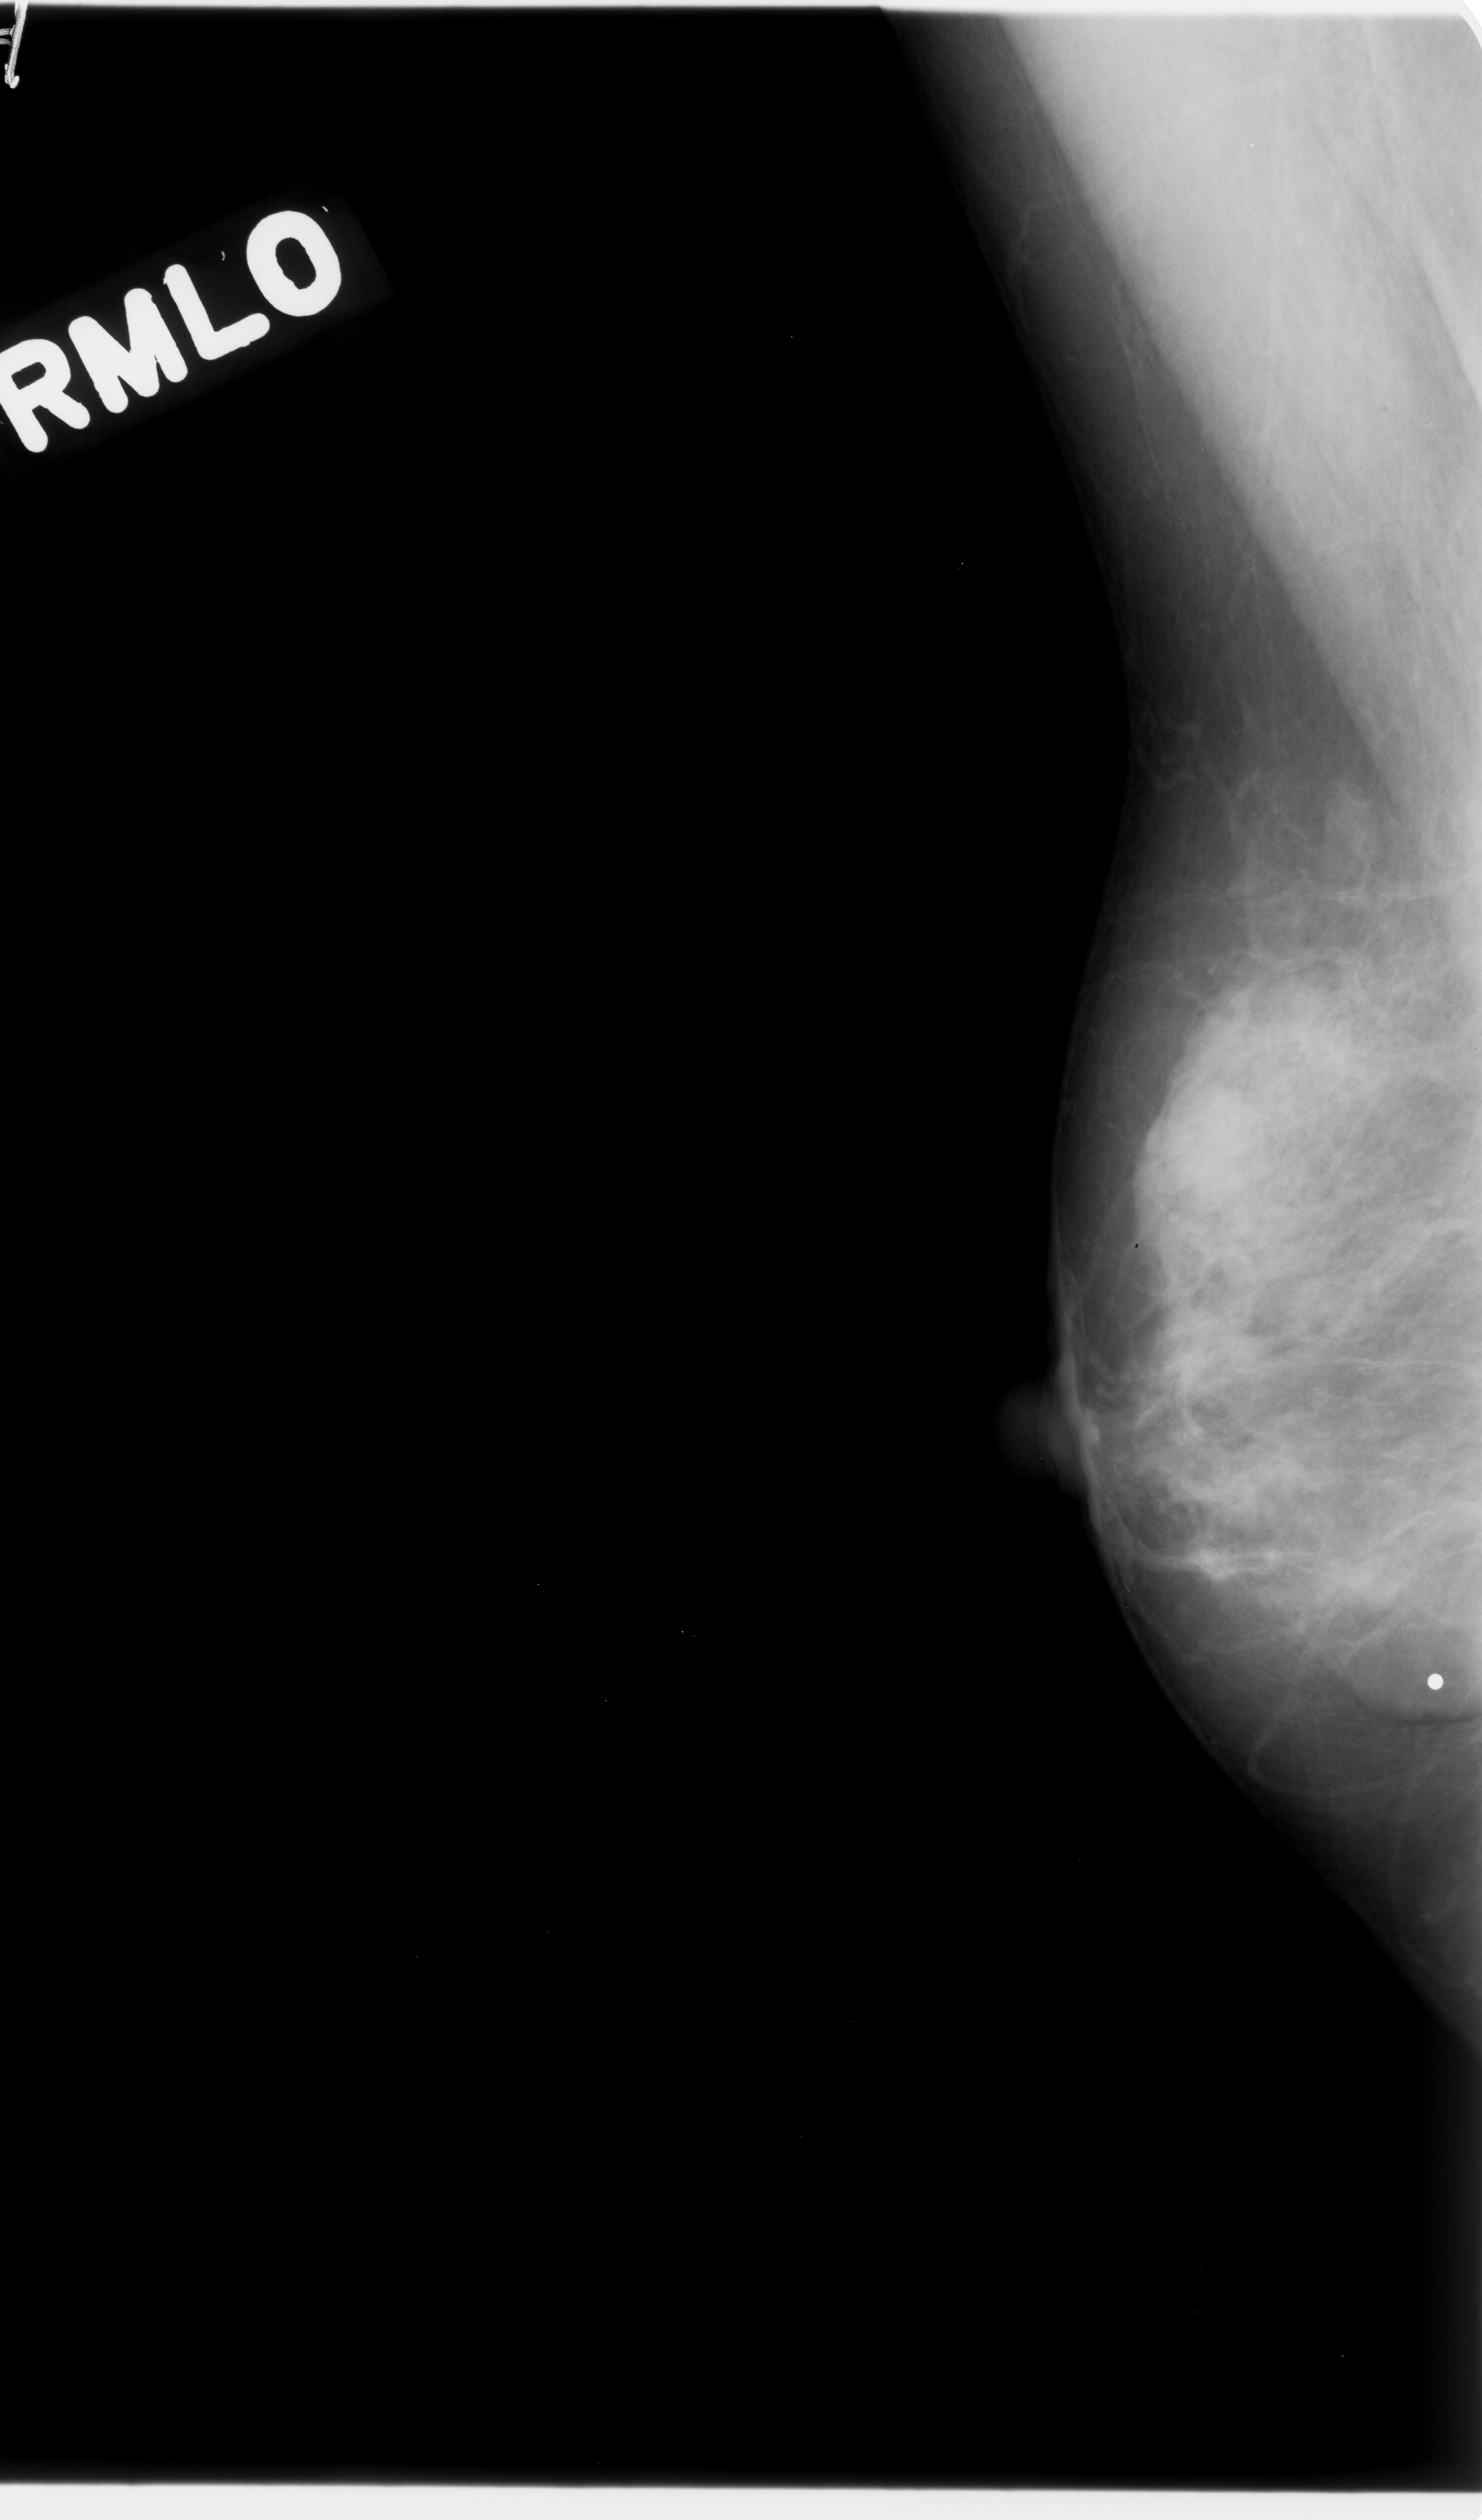
Scanned film-screen mammogram, right breast, MLO view, breast composition: heterogeneously dense (BI-RADS density category 3 of 4).
Finding: mass, shape lobulated, margins microlobulated; BI-RADS assessment category 4; subtlety rating 4 on a 1 (subtle) to 5 (obvious) scale; pathology result (as recorded, not read from the image): benign.